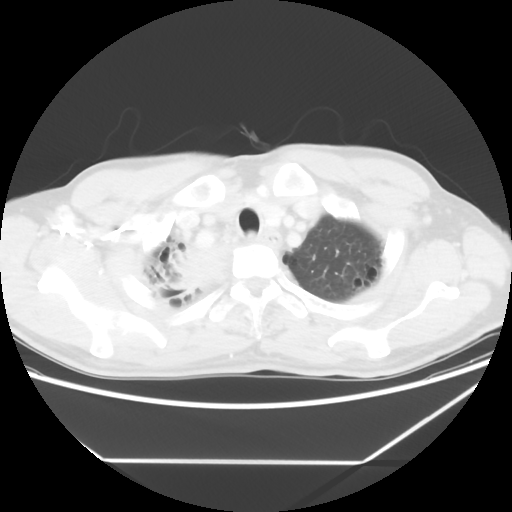
Chest CT, one axial slice; position 54 of 60 along the scan axis; reconstruction kernel STANDARD; 120 kVp; lung window (W 1500 / L -600 HU); 5 mm slice thickness; 512 × 512 image matrix, field of view 367 × 367 mm. Patient: male, 58 years. Case-level facts recorded for this patient, not image findings: clinical TNM (as recorded): T2 N2 M0.
Annotated regions visible in this slice (rectangle marked by the reading radiologist):
- lung tumour (recorded histology: squamous cell carcinoma): box from (x=153, y=242) to (x=231, y=302) px